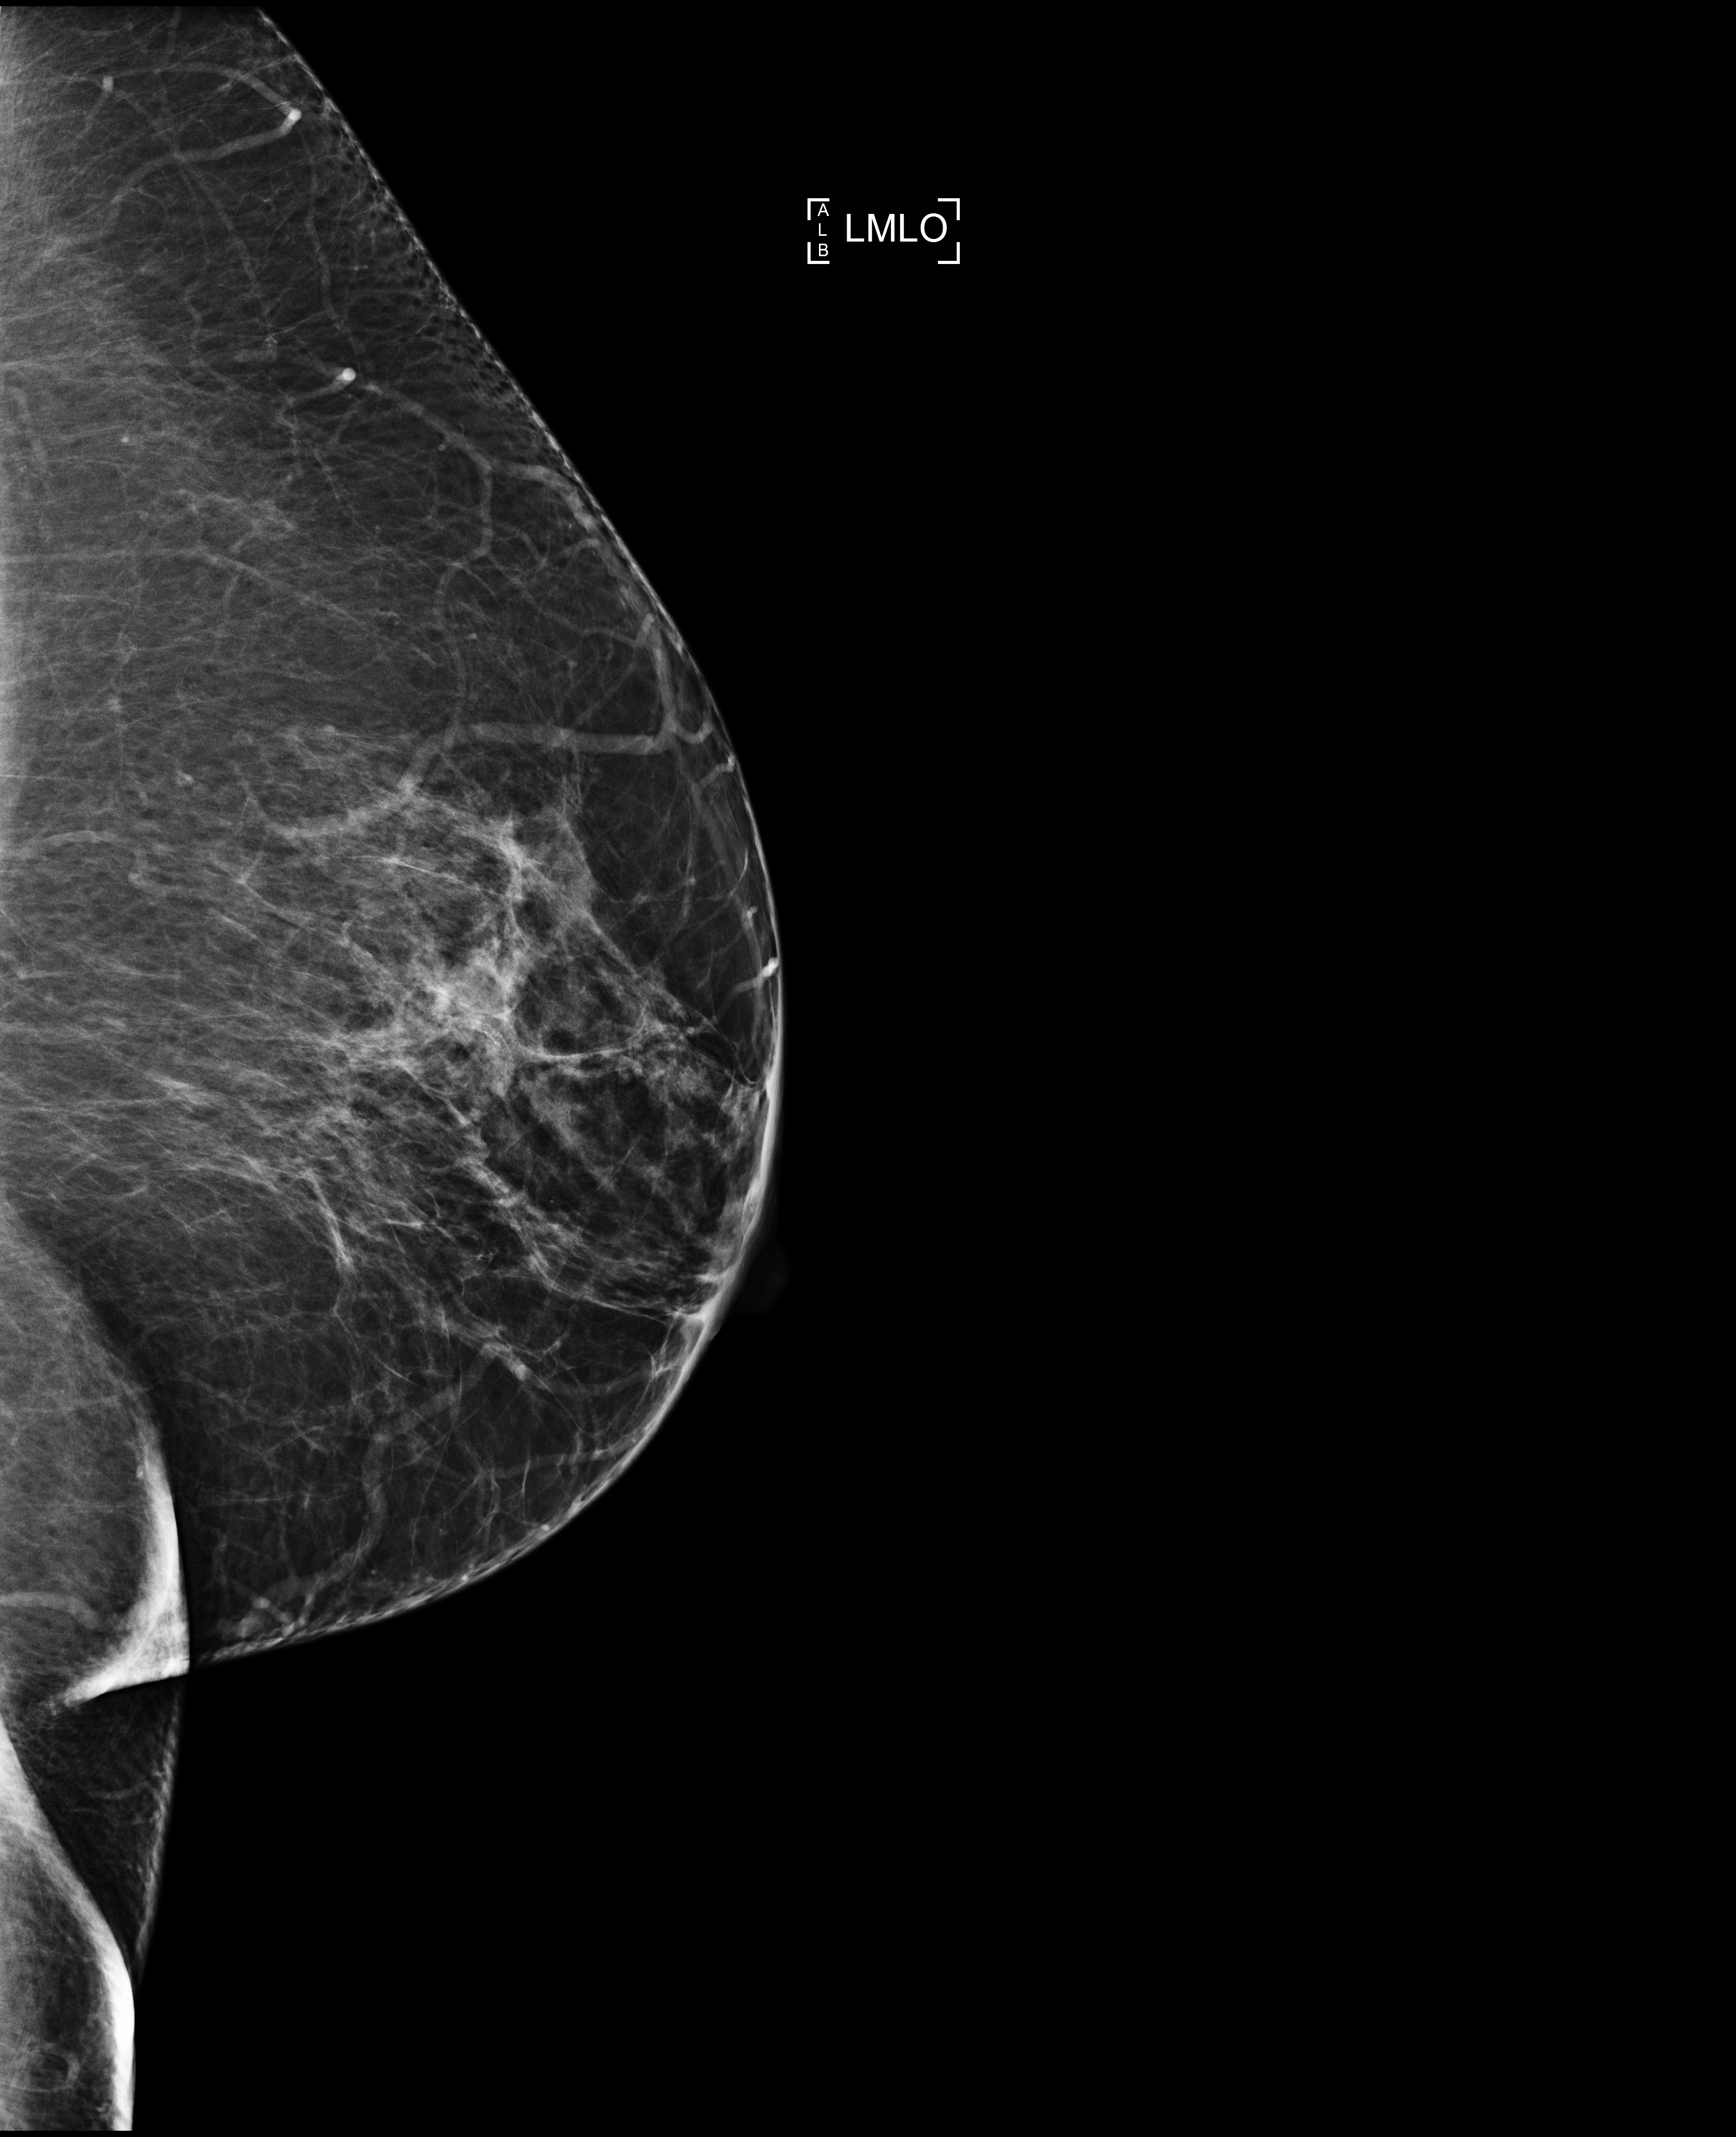
Annual screening mammography examination; compressed breast thickness 75 mm. Patient: female, 62 years.
Image type: full-field digital mammogram. Breast: left. Projection: mediolateral oblique (MLO) view.